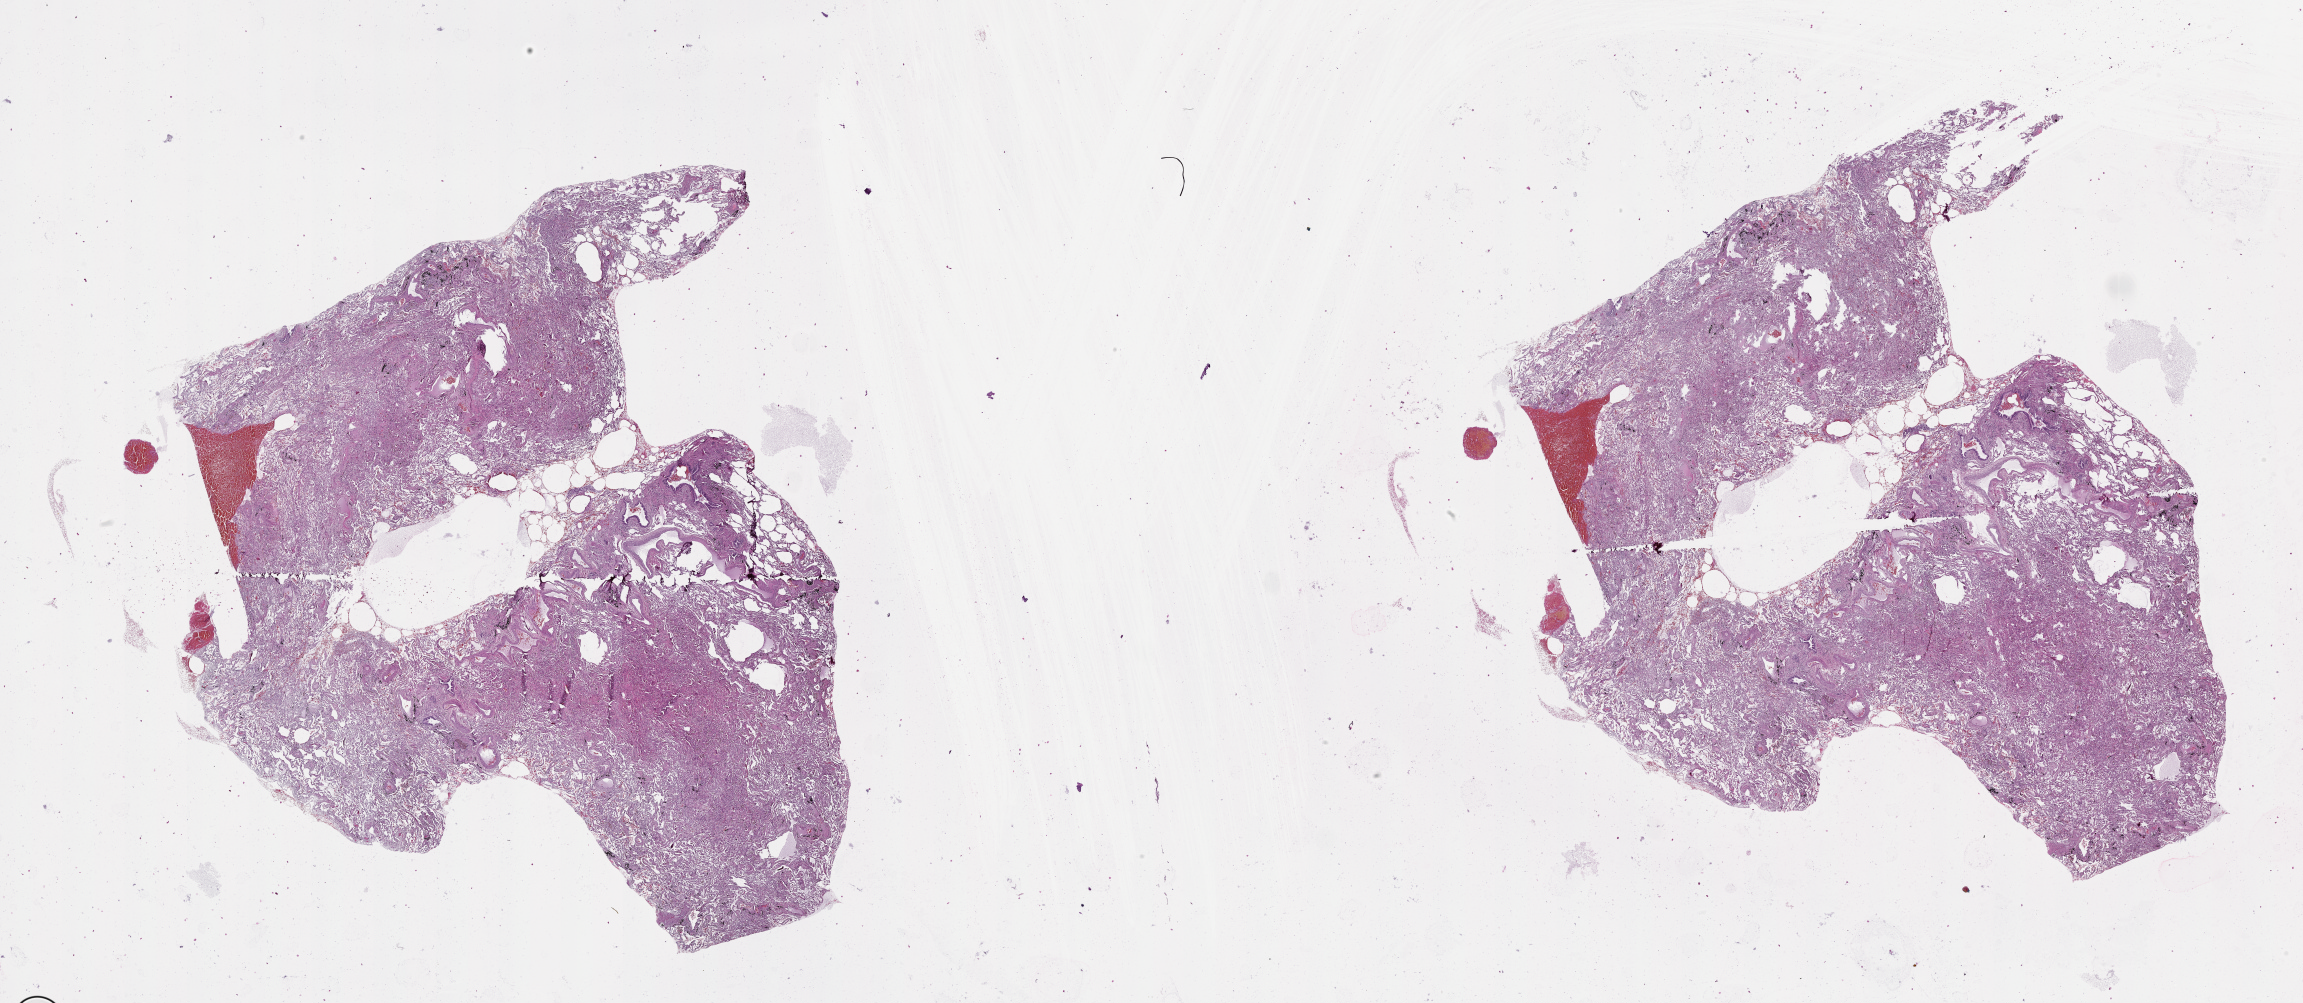
H&E-stained whole-slide image, a low-resolution overview of the entire scanned area, about 37.1 x 16.1 mm (slide scanned at 20x). Normal (non-tumour) tissue sample, lung. Patient: female, age 72 years.
This section: normal (non-tumour) tissue from the same patient. Patient diagnosis (cohort enrolment): squamous cell carcinoma (lung).